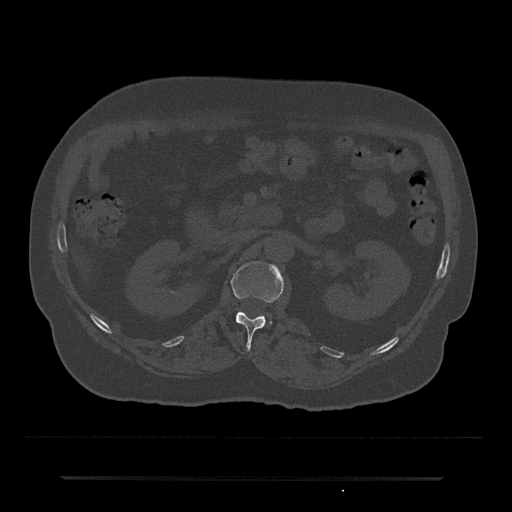
CT including the spine, one axial slice; position 60 of 797 along the scan axis; reconstruction kernel Br40s/3; bone window (W 1800 / L 400 HU); 0.5 mm slice thickness; 512 × 512 image matrix, field of view 437 × 437 mm. Male patient, age 69 years. Case-level facts recorded for this patient, not image findings: primary cancer: prostate.
Outlined on this slice (semi-automatically segmented with operator editing):
- L1 vertebra: bounding box (x1, y1, x2, y2) in pixels: (231, 261, 283, 348)